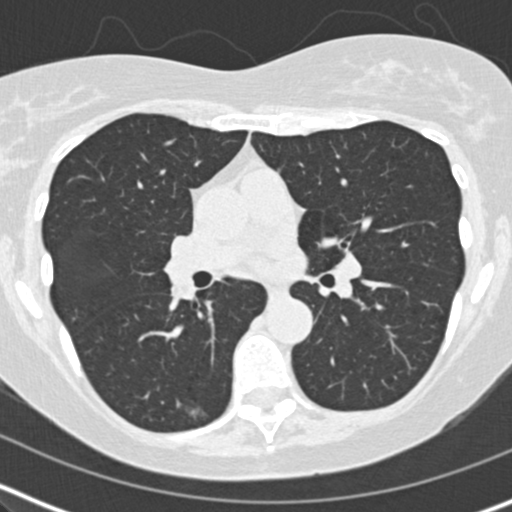
Axial slice from a low-dose chest CT screening exam, second annual screen, lung window (W 1500 / L -600 HU), 2 mm slice thickness, standard (soft-tissue) reconstruction kernel (B30f), slice 76 of 164 in the series, 512 × 512 image matrix, field of view 304 × 304 mm. Female, age 60 years at enrolment. Former smoker at enrolment.
- Expert-annotated lung lesion, box from (x=170, y=393) to (x=221, y=434) px.
- The screening reader recorded 2 non-calcified nodules or masses ≥4 mm on this exam (right middle lobe, right middle lobe); which of them this box marks is not recorded.
- Lung cancer was diagnosed 453 days after this screen (after the third annual screen): acinar cell carcinoma, right lower lobe, moderately differentiated (G2), stage IA (AJCC 6th edition), 10 mm at pathology.